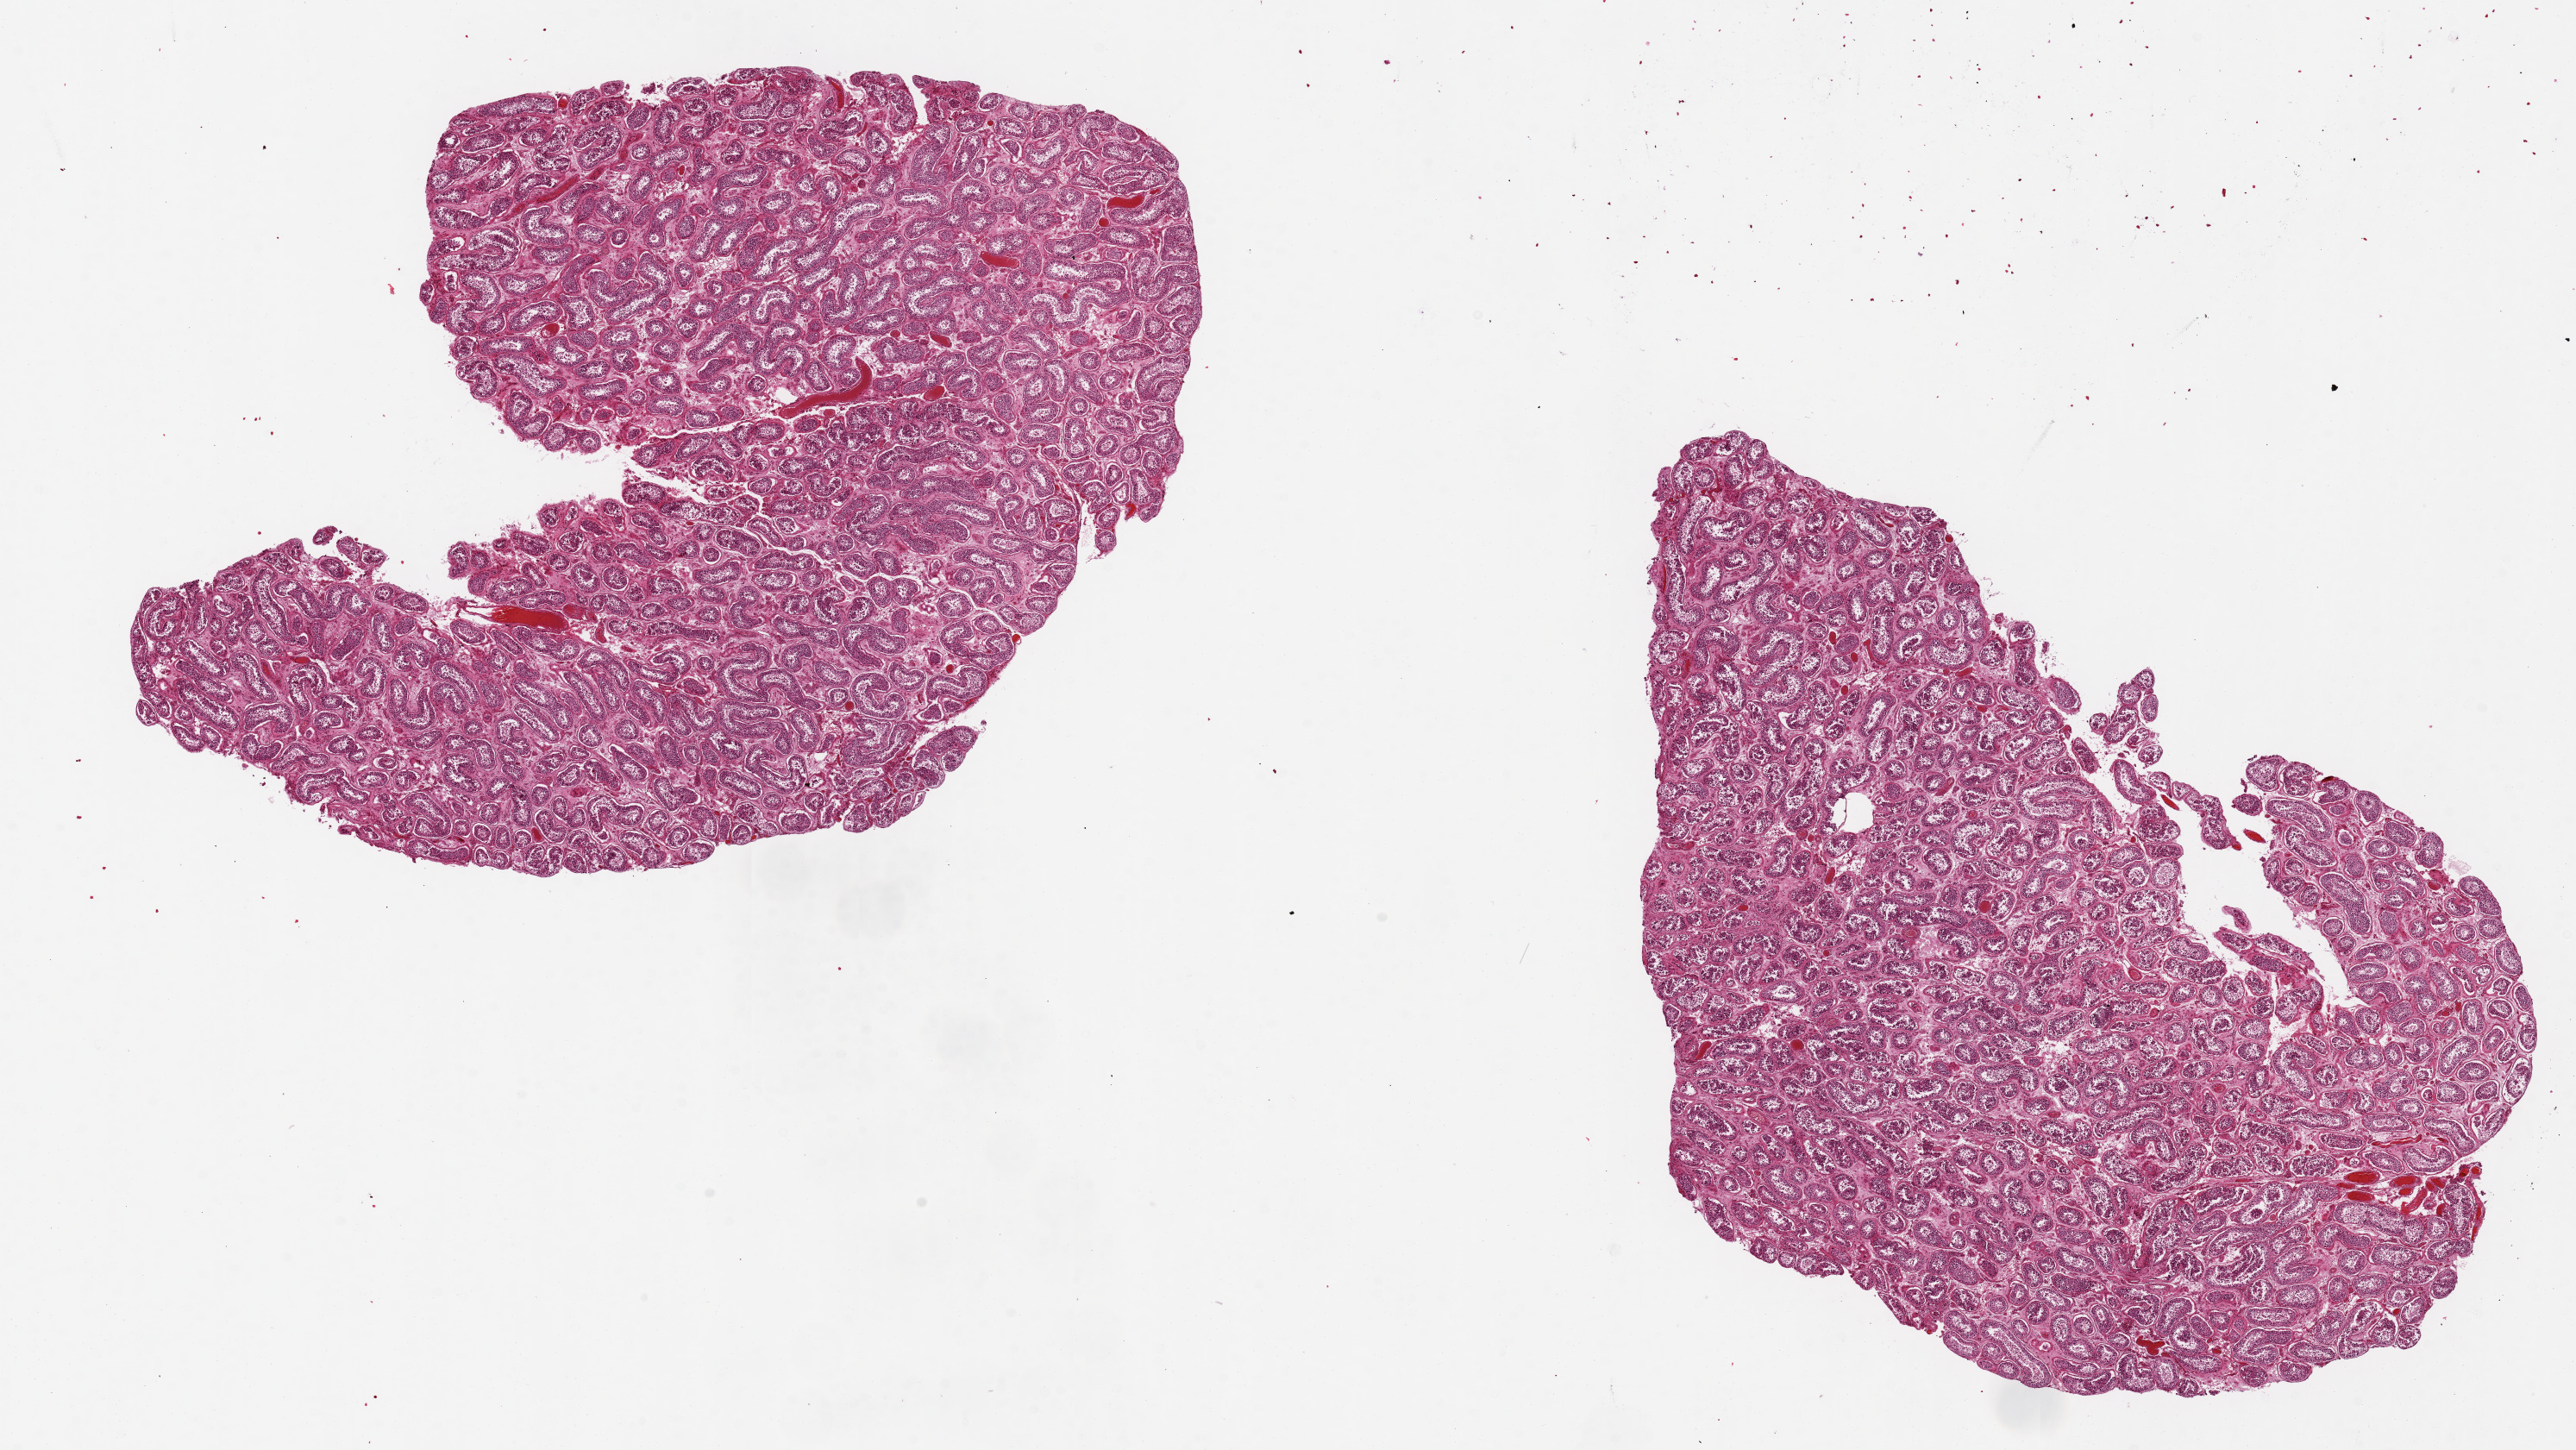
Digitized H&E-stained section, shown as a low-resolution overview of the whole scanned area (about 23.6 x 13.3 mm). PAXgene-fixed, paraffin-embedded tissue. Sampled site (target tissue): testis. Donor tissue sample.
• pathologist's review note for this sample: 2 pieces 10x6 & 6x6 mm; spermatogenesis